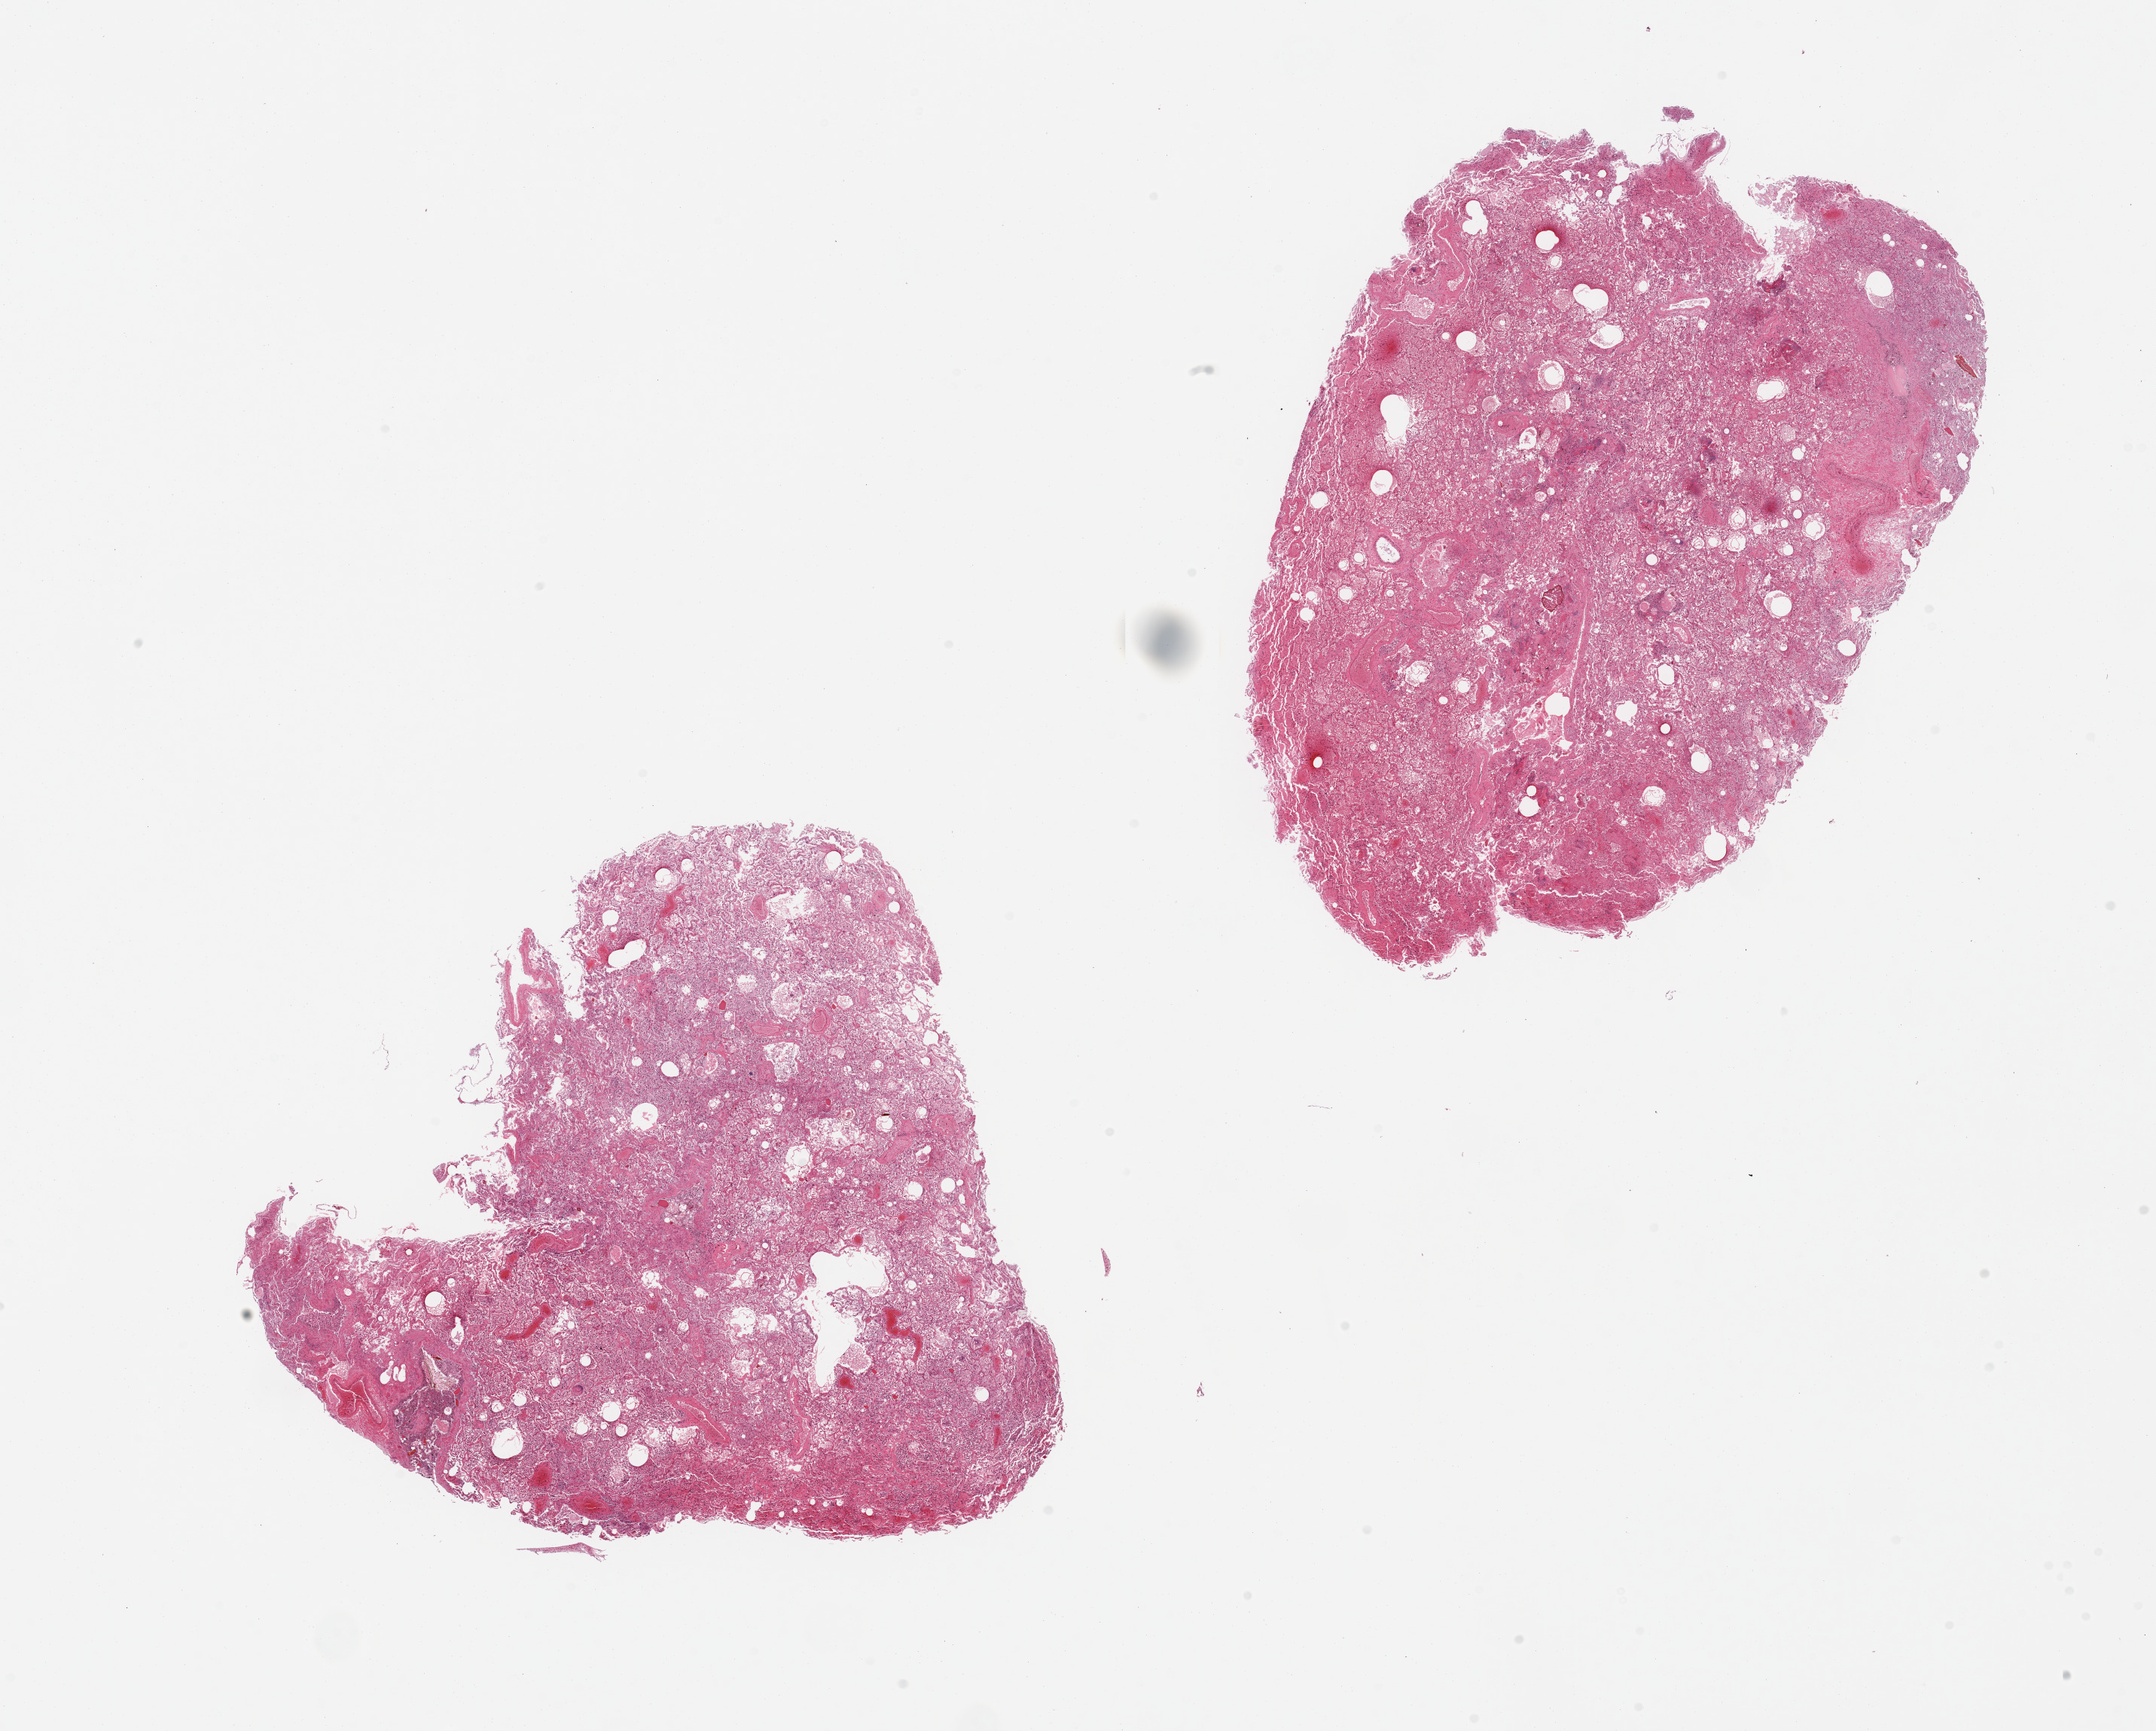
Digitized H&E-stained section — a low-resolution overview of the entire scanned area, about 22.6 x 18.2 mm, PAXgene-fixed, paraffin-embedded tissue, target tissue: lung, donor tissue sample.
- pathologist's review note for this sample: 2 pieces, diffuse marked edema, early acute pneumonia, evidence of aspirated gastric or other contents; foreign/vegetal material